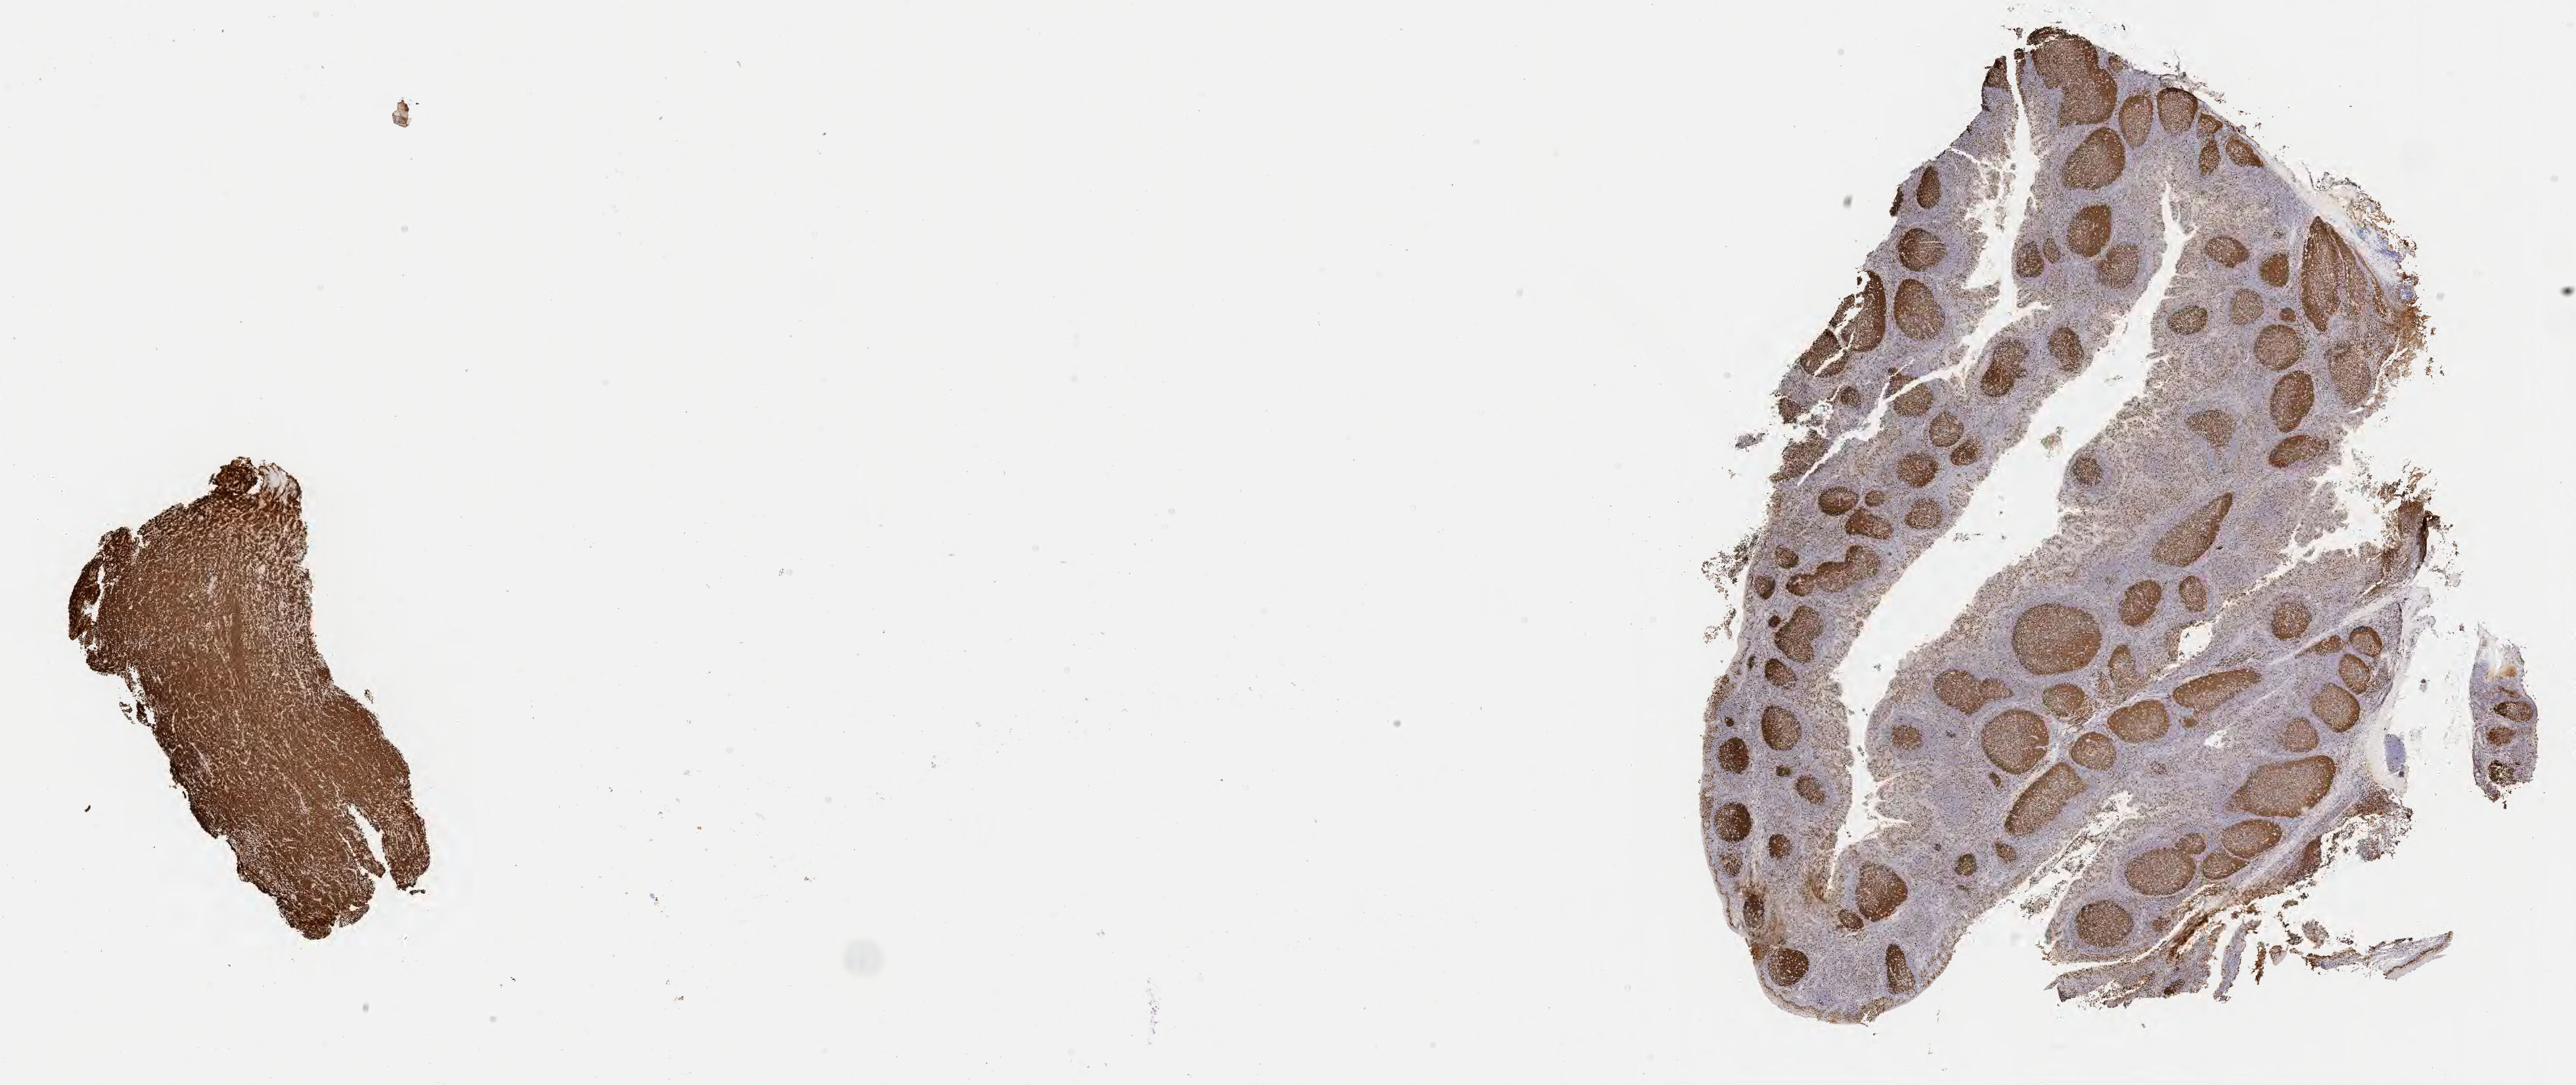
IHC for Ki-67, whole-slide image — whole scanned area (about 31.7 x 13.4 mm) shown as a low-resolution overview, tumor tissue, anatomic site: cranium. Male patient, age 11 years.
* histologic diagnosis: Diffuse large B-cell lymphoma, NOS